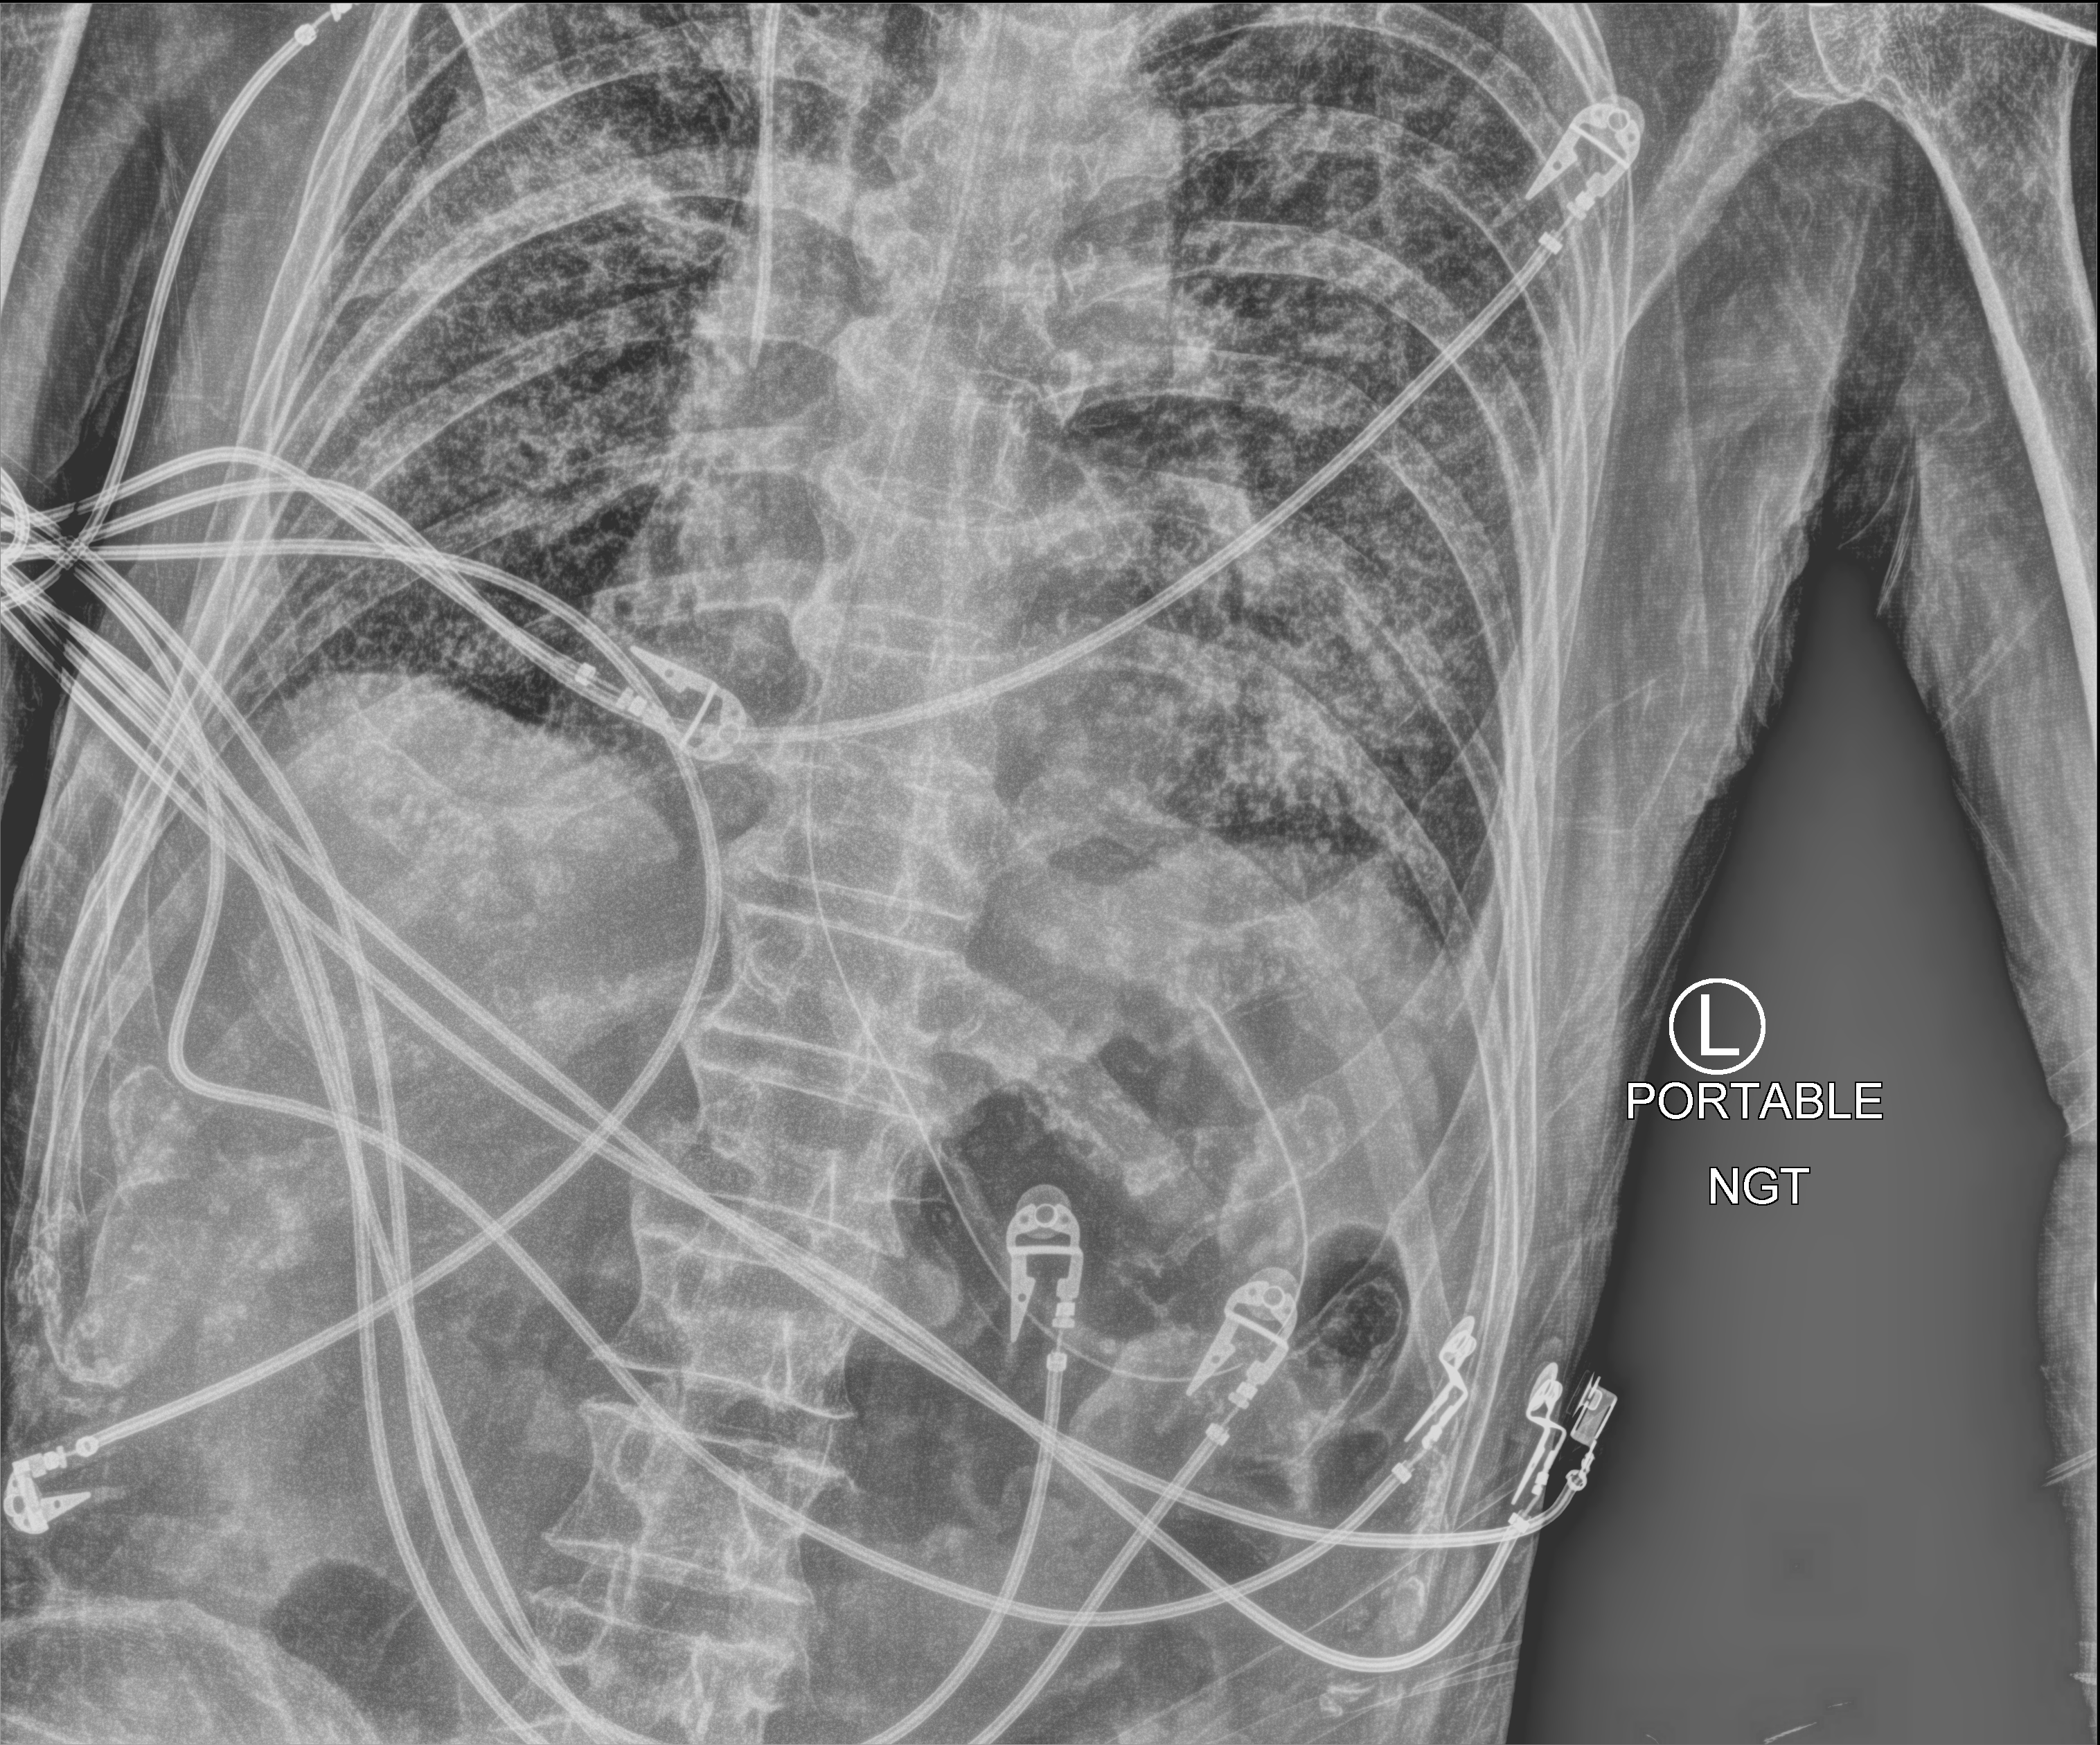
Portable chest radiograph, anteroposterior (AP) projection. Patient hospitalised with COVID-19; male, aged 60–74 years.
Admission-level facts for this patient (not findings on this image; timing relative to this image not recorded):
- admitted to intensive care during this hospital stay: yes
- length of hospital stay: 42 days